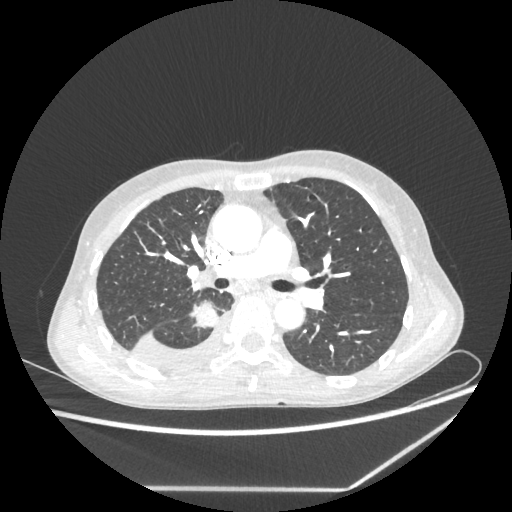
Chest CT, one axial slice; slice 140 of 237 in the series (ordered by position); 80 kVp; lung window (W 1500 / L -600 HU); 1.25 mm slice thickness; 512 × 512 image matrix, field of view 364 × 364 mm. Female patient, age 59 years. Case-level facts recorded for this patient, not image findings: clinical TNM (as recorded): T1c N1 M1.
Outlined on this slice (rectangle marked by the reading radiologist):
- lung tumour (recorded histology: adenocarcinoma): bounding box (x1, y1, x2, y2) in pixels: (190, 298, 219, 328)